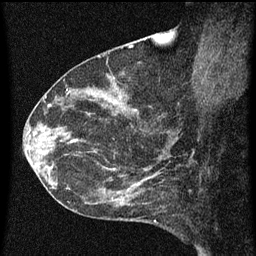
Breast MRI (dynamic contrast-enhanced), one sagittal slice. Dynamic contrast-enhanced series, image 2 of 3 at this slice position (ordered by acquisition). 1.5 T. TE 4.2 ms, TR 8 ms. 2 mm slice thickness. 256 × 256 image matrix. Female patient, age 54 years.
Structures marked on this image (semi-automatic segmentation, software-assisted and operator-edited):
- analysis volume of interest (the breast-tissue region the enhancement analysis was run in; not a lesion): bounding box (x1, y1, x2, y2) in pixels: (49, 138, 164, 209)
- tumour enhancement mask (voxels above the 70 % enhancement threshold inside the analysis volume of interest): (86, 142, 162, 205)